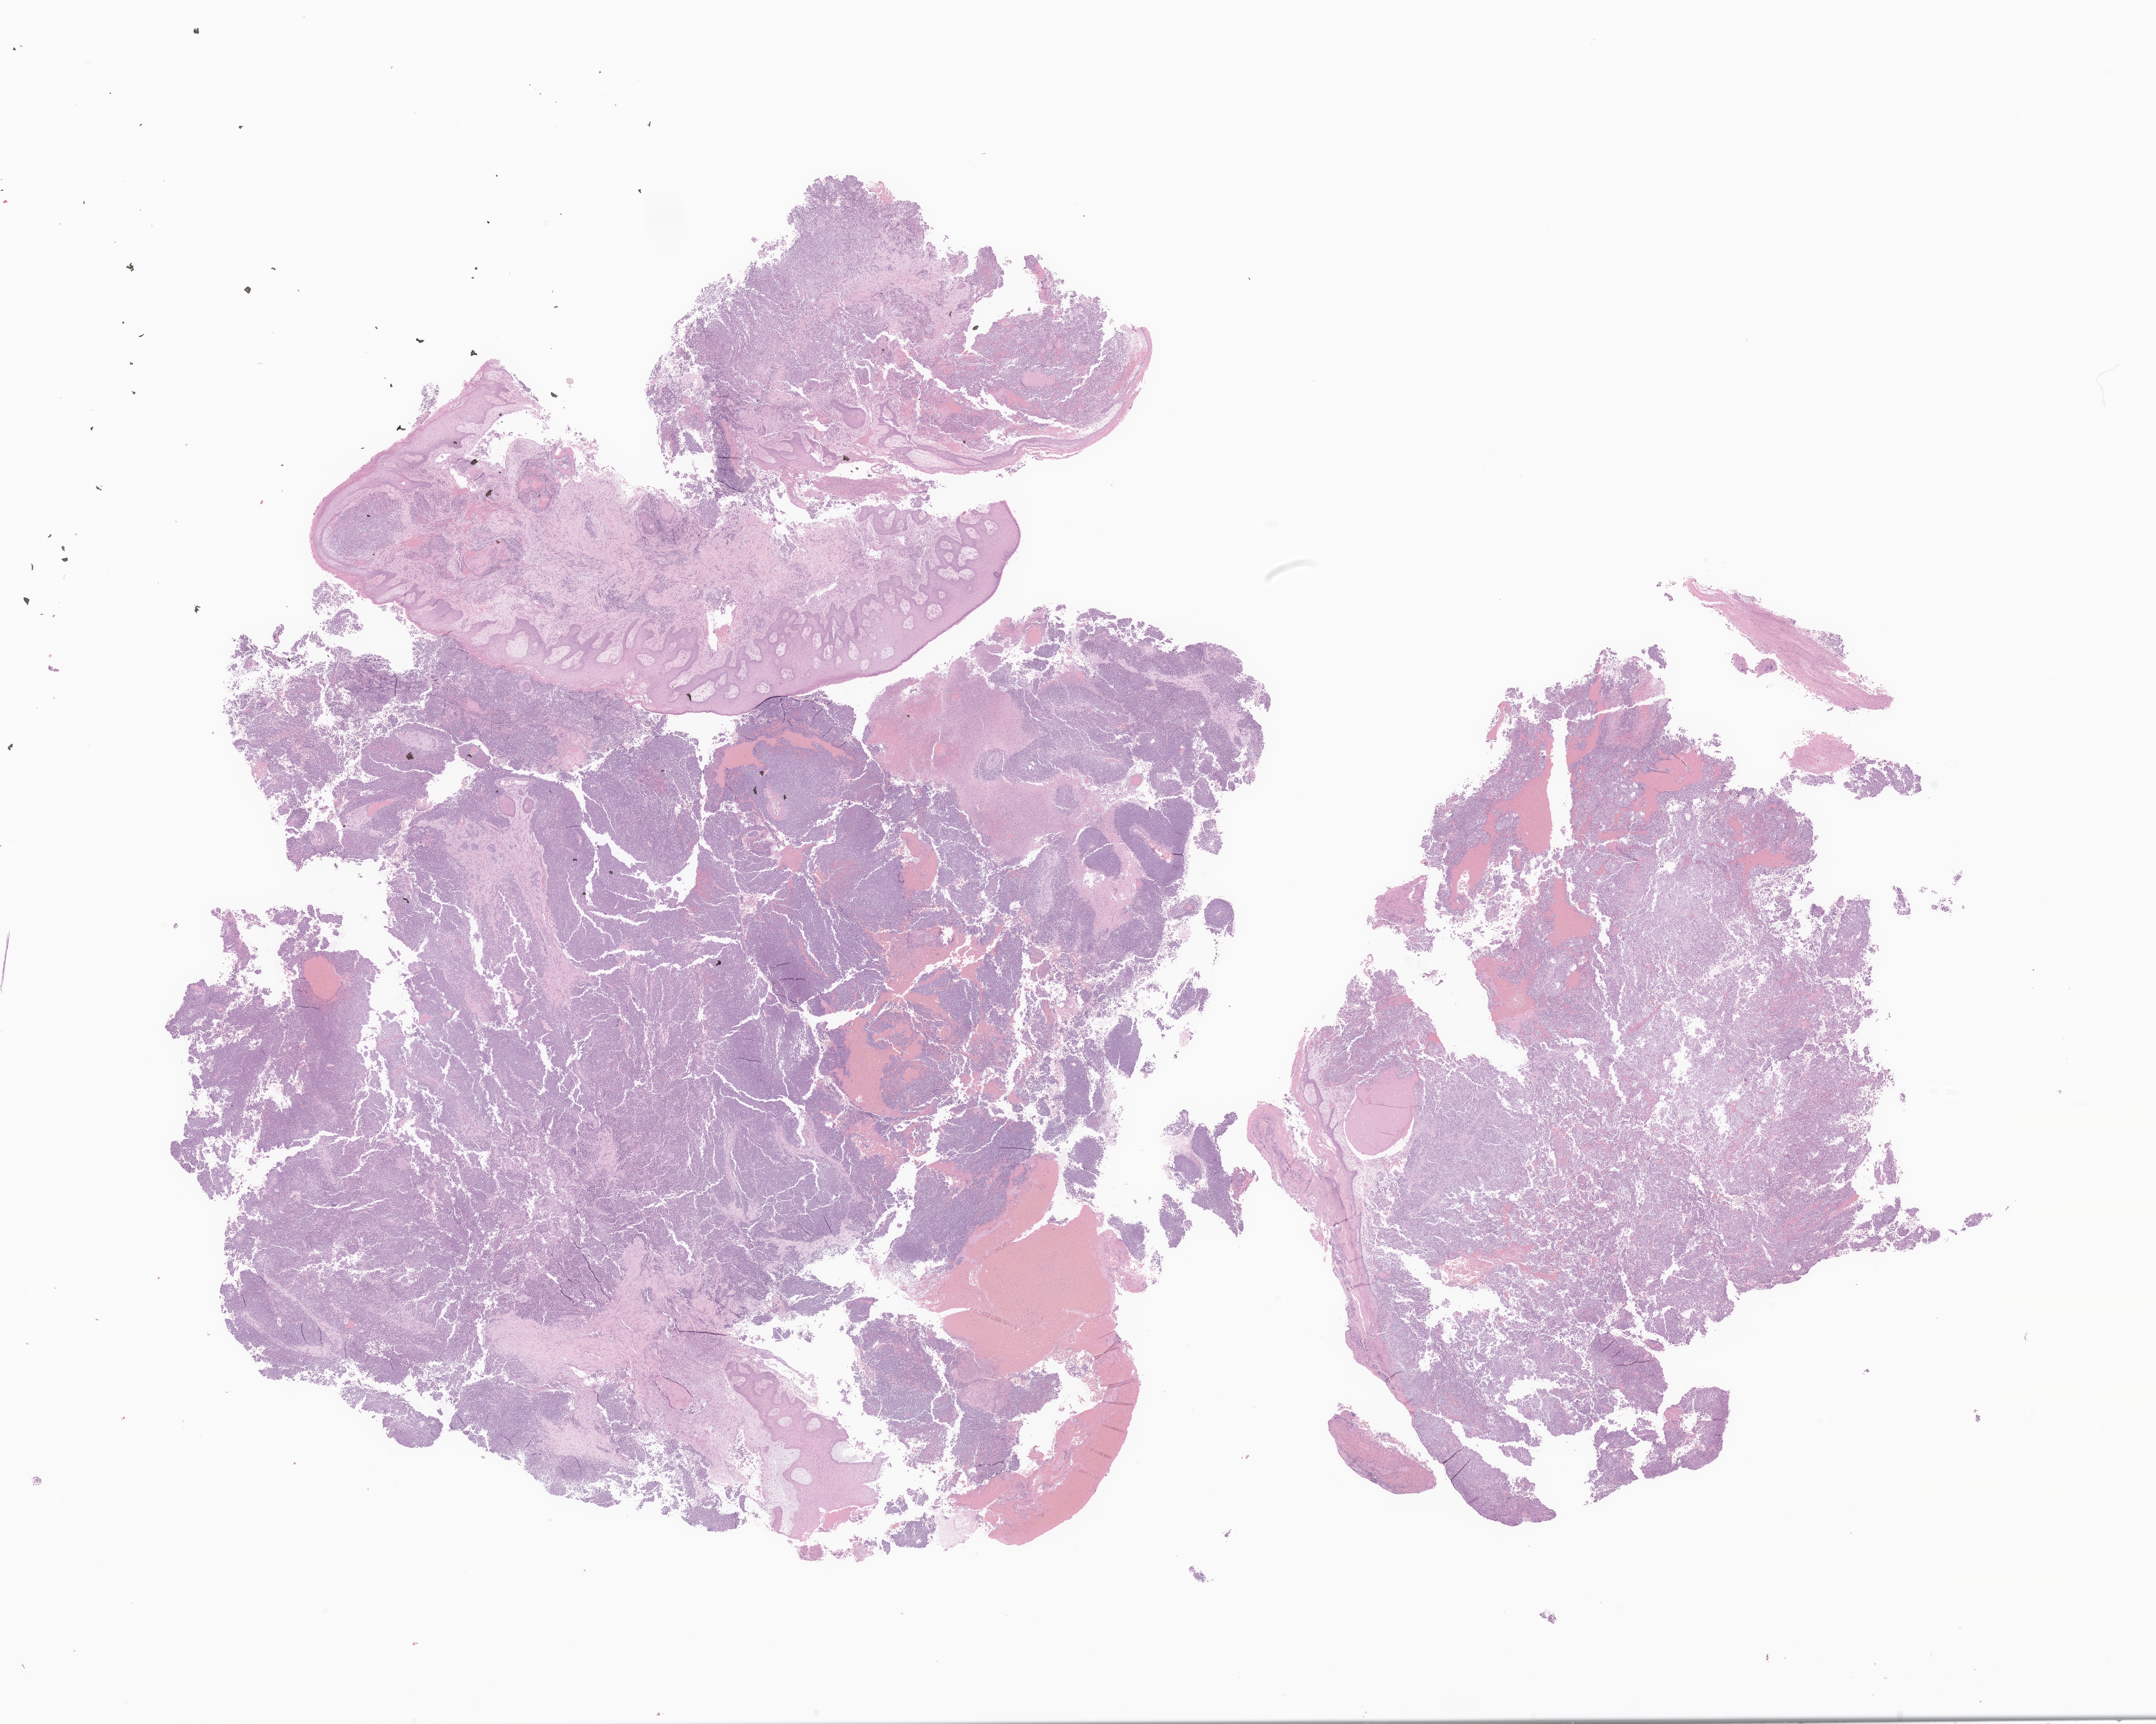
Digitized haematoxylin and eosin-stained section of tumor tissue from the soft tissue — low-resolution overview of the scanned area, about 24.9 x 19.9 mm; formalin-fixed, paraffin-embedded (FFPE) tissue. Female patient, age 200 months (16 years 8 months).
Recorded diagnosis: Desmoplastic small round cell tumor.